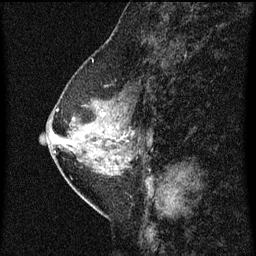
Breast MRI (dynamic contrast-enhanced), one sagittal slice. Slice 25 of 60 in the series (ordered by position). Dynamic contrast-enhanced series, image 2 of 3 at this slice position (ordered by acquisition). 1.5 T. TE 4.2 ms, TR 8 ms. 2 mm slice thickness. 256 × 256 image matrix, field of view 180 × 180 mm. Patient: female, 47 years.
Outlined on this slice (semi-automatic segmentation, software-assisted and operator-edited):
- analysis volume of interest (the breast-tissue region the enhancement analysis was run in; not a lesion): bounding box <54,80,146,187> (left, top, right, bottom; pixels)
- tumour enhancement mask (voxels above the 70 % enhancement threshold inside the analysis volume of interest): <55,110,135,161>